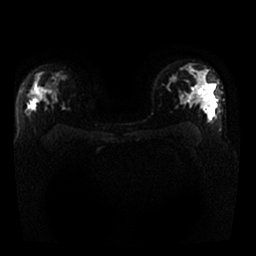
Breast MRI, one axial slice. Slice 18 of 25 in the series (ordered by position). Diffusion-weighted series; image 2 of 4 stored at this slice position (different b-values; order by instance number). 1.5 T. 256 × 256 image matrix, field of view 340 × 340 mm. Female patient.
Annotated regions visible in this slice (outlined manually by an expert reader):
- tumour on diffusion-weighted imaging: bounding box (x1, y1, x2, y2) in pixels: (30, 91, 34, 96)